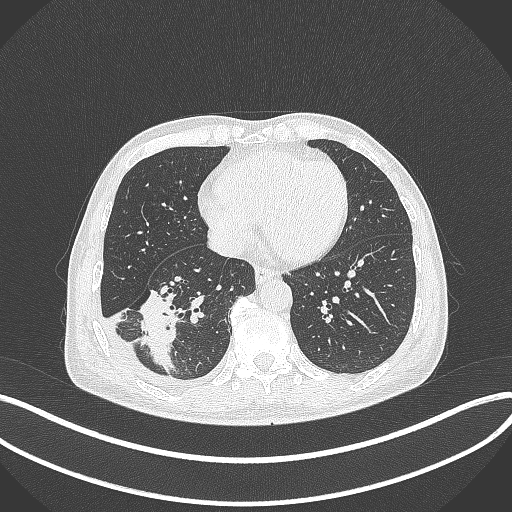
Chest CT, one axial slice. 120 kVp. Lung window (W 1500 / L -600 HU). 1 mm slice thickness. 512 × 512 image matrix. Male patient, age 64 years. Case-level facts recorded for this patient, not image findings: clinical TNM (as recorded): T3 N0 M0; histopathological grade: G2-3.
Structures marked on this image (rectangle marked by the reading radiologist):
- lung tumour (recorded histology: adenocarcinoma): bounding box [x1, y1, x2, y2] px = [137, 288, 177, 380]